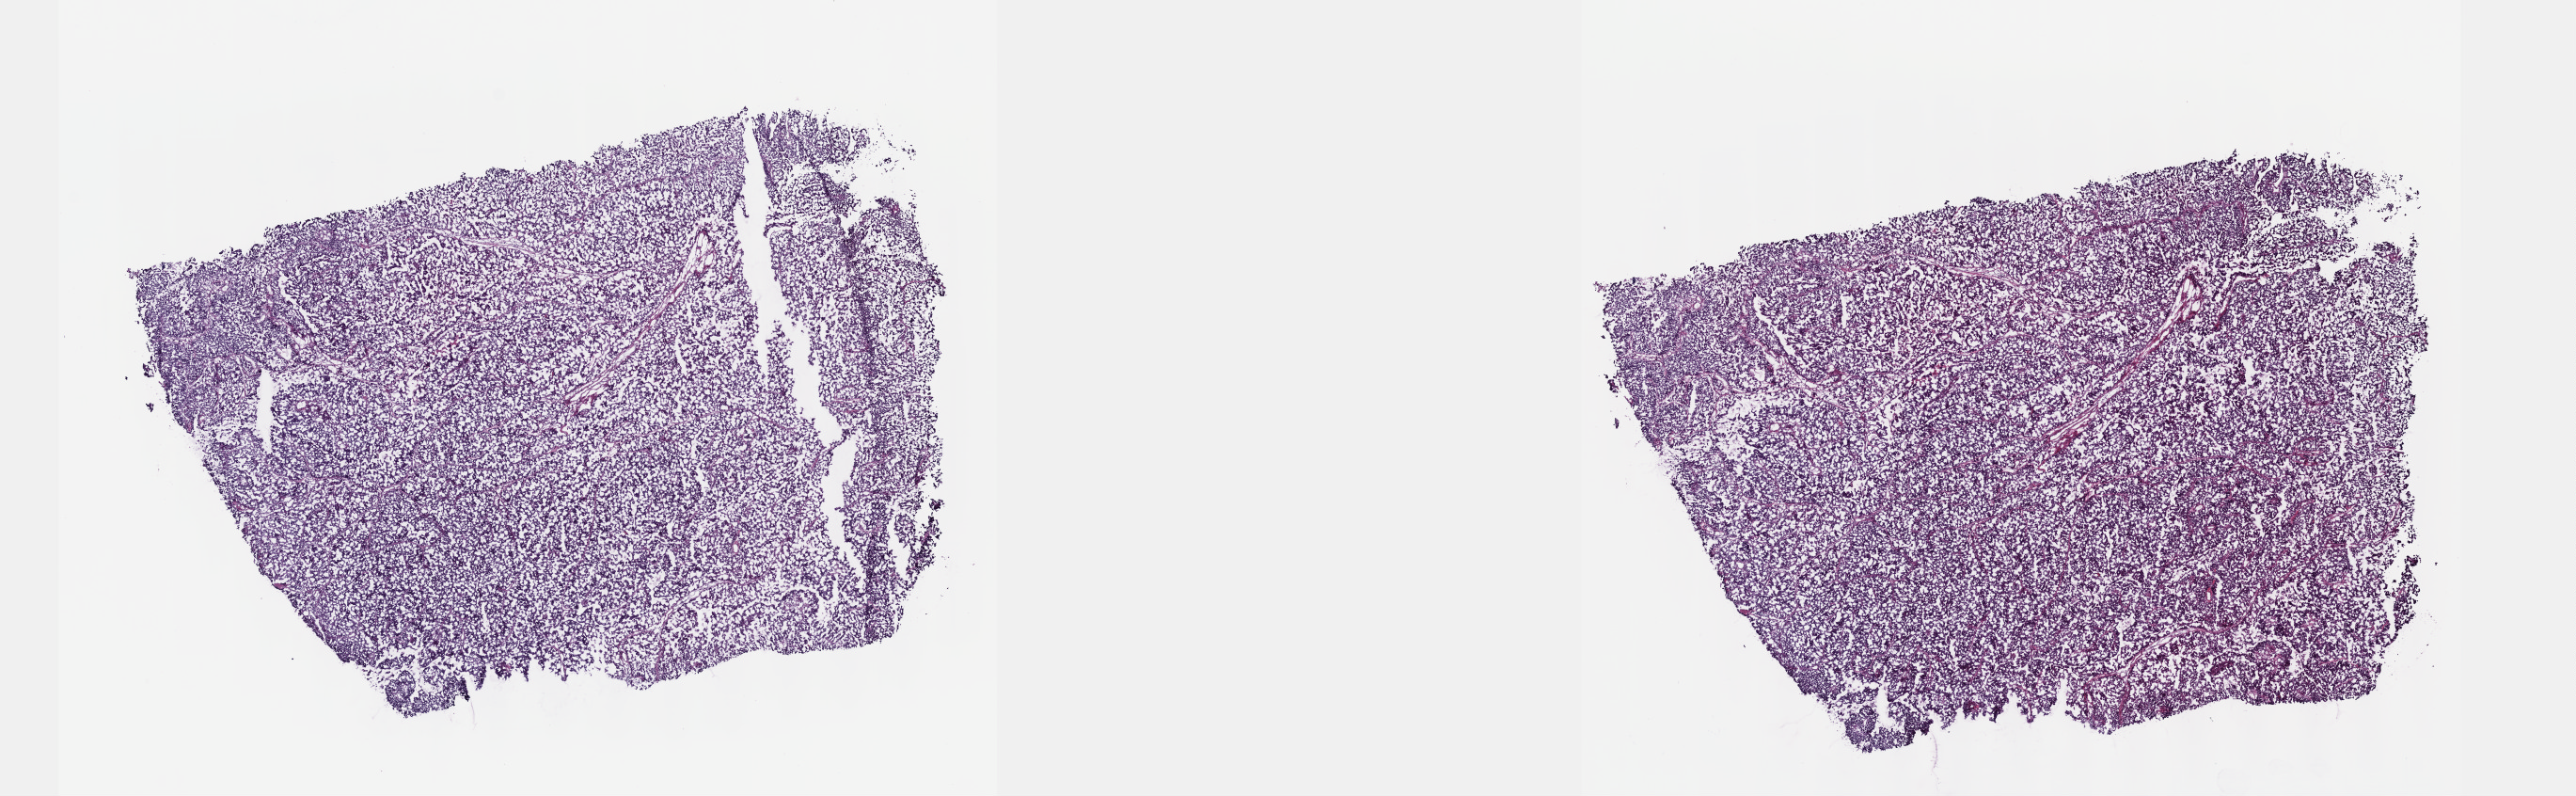
Whole-slide histology image, Hematoxylin and eosin (H&E) stained — whole scanned area (about 22.1 x 6.8 mm, acquisition: 40x scan) shown as a low-resolution overview. Frozen section from the top of the tissue portion. Bladder, primary tumour sample. Male patient; age at initial diagnosis 59 years. Slide review estimates, as recorded: tumour cells 90%, tumour nuclei 95%.
Diagnosis: Transitional cell carcinoma.